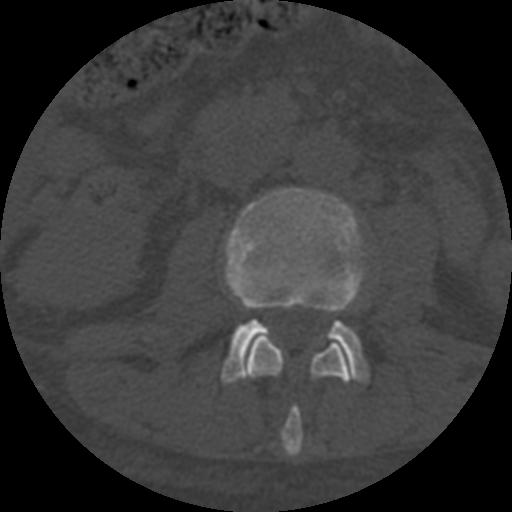
CT including the spine, one axial slice. Position 245 of 708 along the scan axis. Reconstruction kernel STANDARD. 120 kVp. One of 3 acquisitions stored at this slice position. Bone window (W 1800 / L 400 HU). 1.25 mm slice thickness. 512 × 512 image matrix. Patient age 55 years. Case-level facts recorded for this patient, not image findings: primary cancer: colon; vertebrae with lytic lesions (as recorded): T12, L1, L5.
Outlined on this slice (semi-automatically segmented with operator editing):
- L2 vertebra: bounding box (x1, y1, x2, y2) in pixels: (245, 337, 353, 457)
- L3 vertebra: (222, 188, 367, 383)